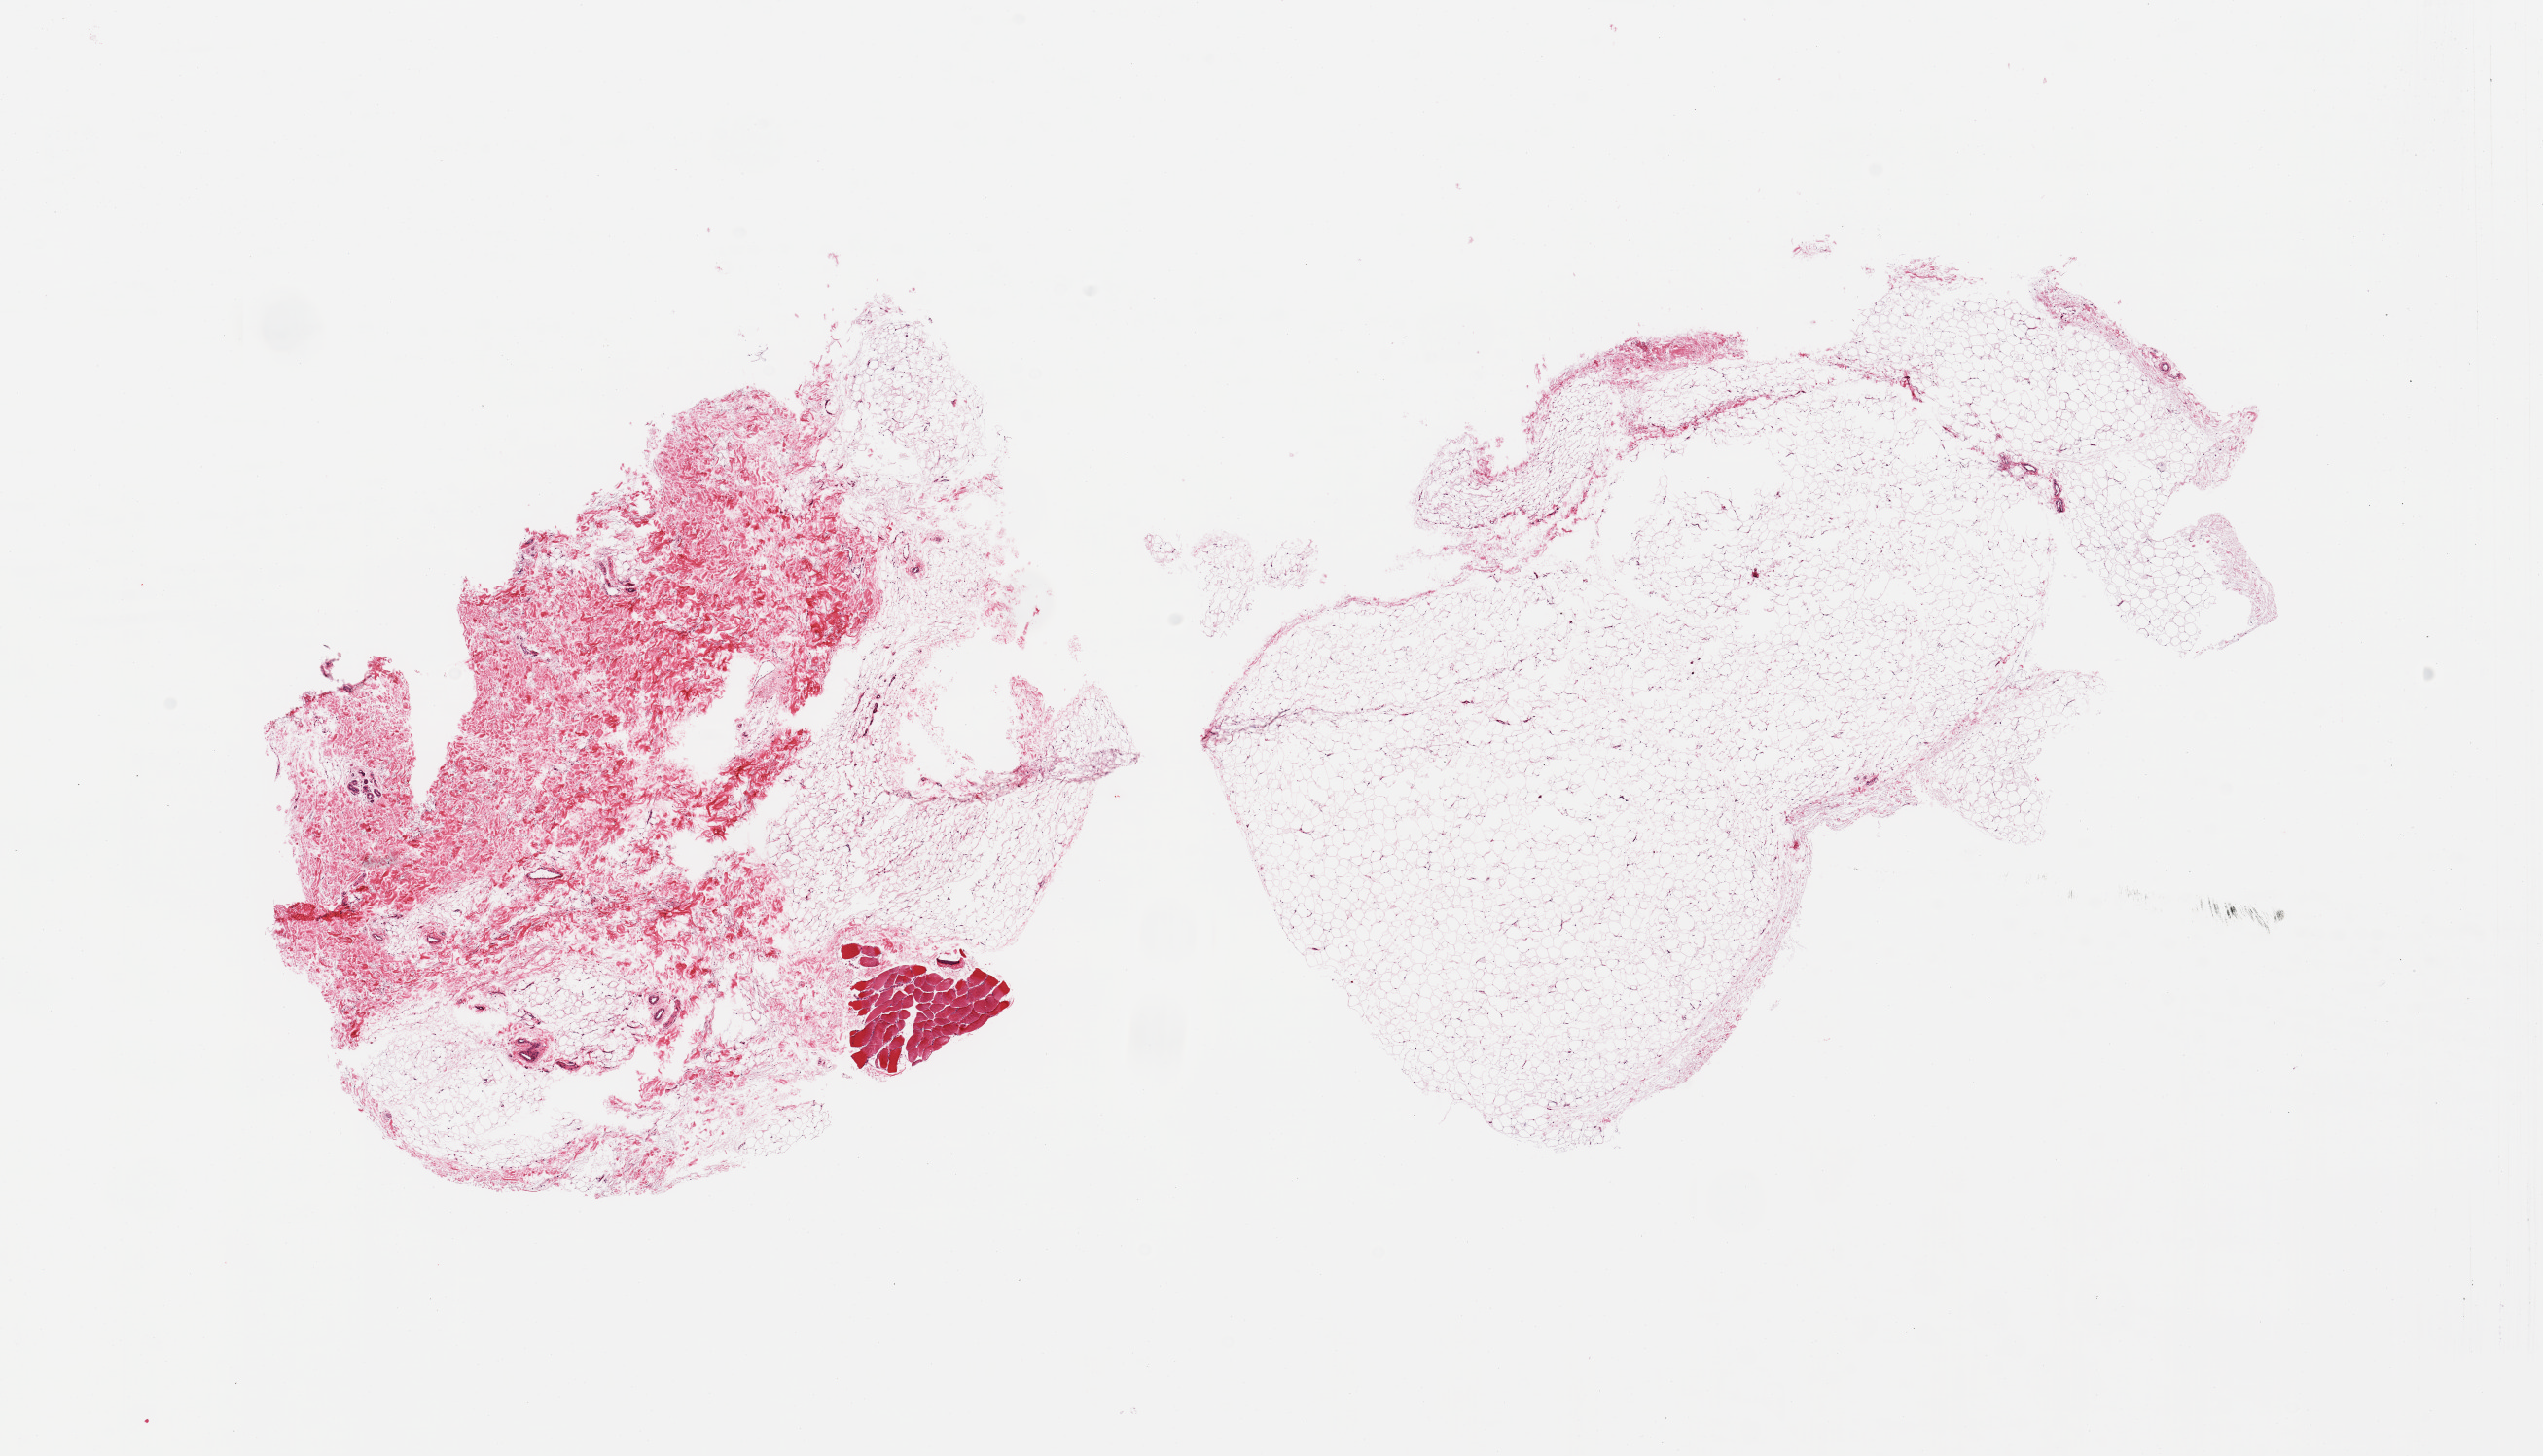
Hematoxylin and eosin (H&E) whole-slide image — low-resolution overview of the scanned area, about 20.7 x 11.8 mm (acquisition: 20x scan), PAXgene-fixed paraffin-embedded (PFPE) section, sampled site (target tissue): adipose tissue, donor tissue sample.
Review note (as recorded): 2 pieces, fascia/skeletal muscle is ~30 % of specimen.